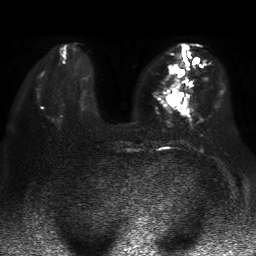
Breast MRI, one axial slice. Slice 16 of 50 in the series (ordered by position). Diffusion-weighted series; image 2 of 4 stored at this slice position (different b-values; order by instance number). 1.5 T. 256 × 256 image matrix, field of view 360 × 360 mm. Female patient.
Annotated regions visible in this slice (outlined manually by an expert reader):
- tumour on diffusion-weighted imaging: box from (x=168, y=65) to (x=183, y=106) px